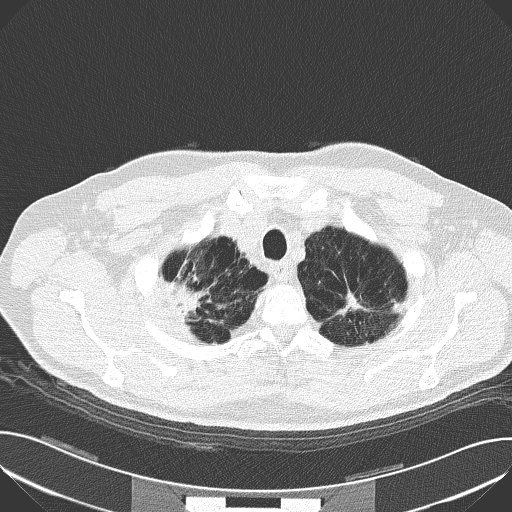
Low-dose screening chest CT, axial slice. Baseline annual screen. Lung window (W 1500 / L -600 HU). Slice 17 of 159 in the series. Male participant, aged 59 years at enrolment. Current smoker at enrolment.
Lesion marked by an expert reader, bounding box <155,259,224,333> (left, top, right, bottom; pixels). The screening reader recorded 4 non-calcified nodules or masses ≥4 mm on this exam (right upper lobe, left upper lobe, right upper lobe, left upper lobe); which of them this box marks is not recorded. Lung cancer was diagnosed 44 days after this screen: squamous cell carcinoma, NOS, right upper lobe, moderately differentiated (G2), stage IA (AJCC 6th edition), 30 mm at pathology.